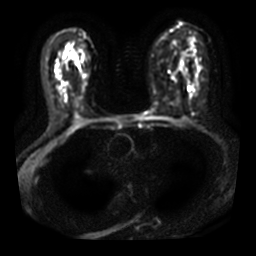
Breast MRI, one axial slice. Position 20 of 40 along the scan axis. Diffusion-weighted series; image 2 of 4 stored at this slice position (different b-values; order by instance number). 3 T. 256 × 256 image matrix, field of view 320 × 320 mm. Female patient.
Structures marked on this image (expert manual segmentation):
- tumour on diffusion-weighted imaging: bounding box <77,63,80,66> (left, top, right, bottom; pixels)